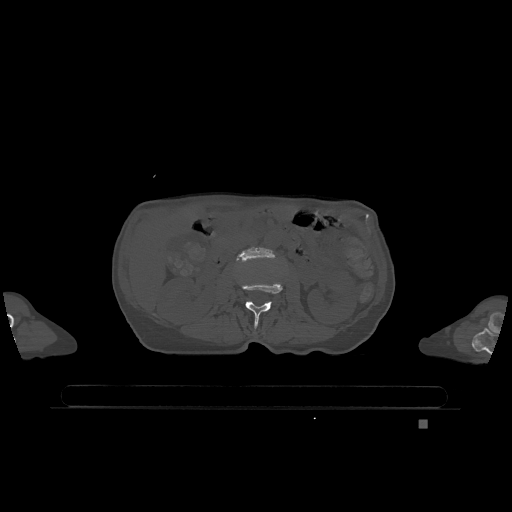
CT including the spine, one axial slice; slice 402 of 1317 in the series (ordered by position); bone window (W 1800 / L 400 HU); 0.5 mm slice thickness; 512 × 512 image matrix. Female patient, age 74 years. Case-level facts recorded for this patient, not image findings: primary cancer: lung; vertebrae with lytic lesions (as recorded): T1, T4, T5, T6, L4, L5.
Annotated regions visible in this slice (semi-automatic segmentation, software-assisted and operator-edited):
- L2 vertebra: bounding box (x1, y1, x2, y2) in pixels: (242, 282, 283, 329)
- L3 vertebra: (237, 247, 273, 261)